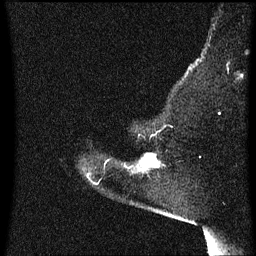
Breast MRI (dynamic contrast-enhanced), one sagittal slice; position 49 of 60 along the scan axis; dynamic contrast-enhanced series, image 2 of 3 at this slice position (ordered by acquisition); 1.5 T; TE 4.2 ms, TR 8.4 ms; 2 mm slice thickness; 256 × 256 image matrix, field of view 200 × 200 mm. Female patient, age 54 years. Case-level facts recorded for this patient, not image findings: setting: breast cancer imaged before/during neoadjuvant chemotherapy; receptor status: HR-positive, HER2-negative.
Annotated regions visible in this slice (semi-automatically segmented with operator editing):
- analysis volume of interest (the breast-tissue region the enhancement analysis was run in; not a lesion): bounding box [x1, y1, x2, y2] px = [133, 154, 161, 175]
- tumour enhancement mask (voxels above the 70 % enhancement threshold inside the analysis volume of interest): [143, 154, 159, 167]